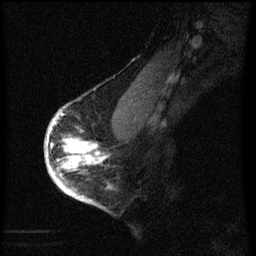
Breast MRI (dynamic contrast-enhanced), one sagittal slice. Position 44 of 60 along the scan axis. Dynamic contrast-enhanced series, image 2 of 3 at this slice position (ordered by acquisition). 1.5 T. TE 4.2 ms, TR 8 ms. 2 mm slice thickness. 256 × 256 image matrix. Female patient, age 56 years.
Outlined on this slice (semi-automatic segmentation, software-assisted and operator-edited):
- analysis volume of interest (the breast-tissue region the enhancement analysis was run in; not a lesion): bounding box [x1, y1, x2, y2] px = [46, 110, 109, 193]
- tumour enhancement mask (voxels above the 70 % enhancement threshold inside the analysis volume of interest): [46, 114, 103, 193]